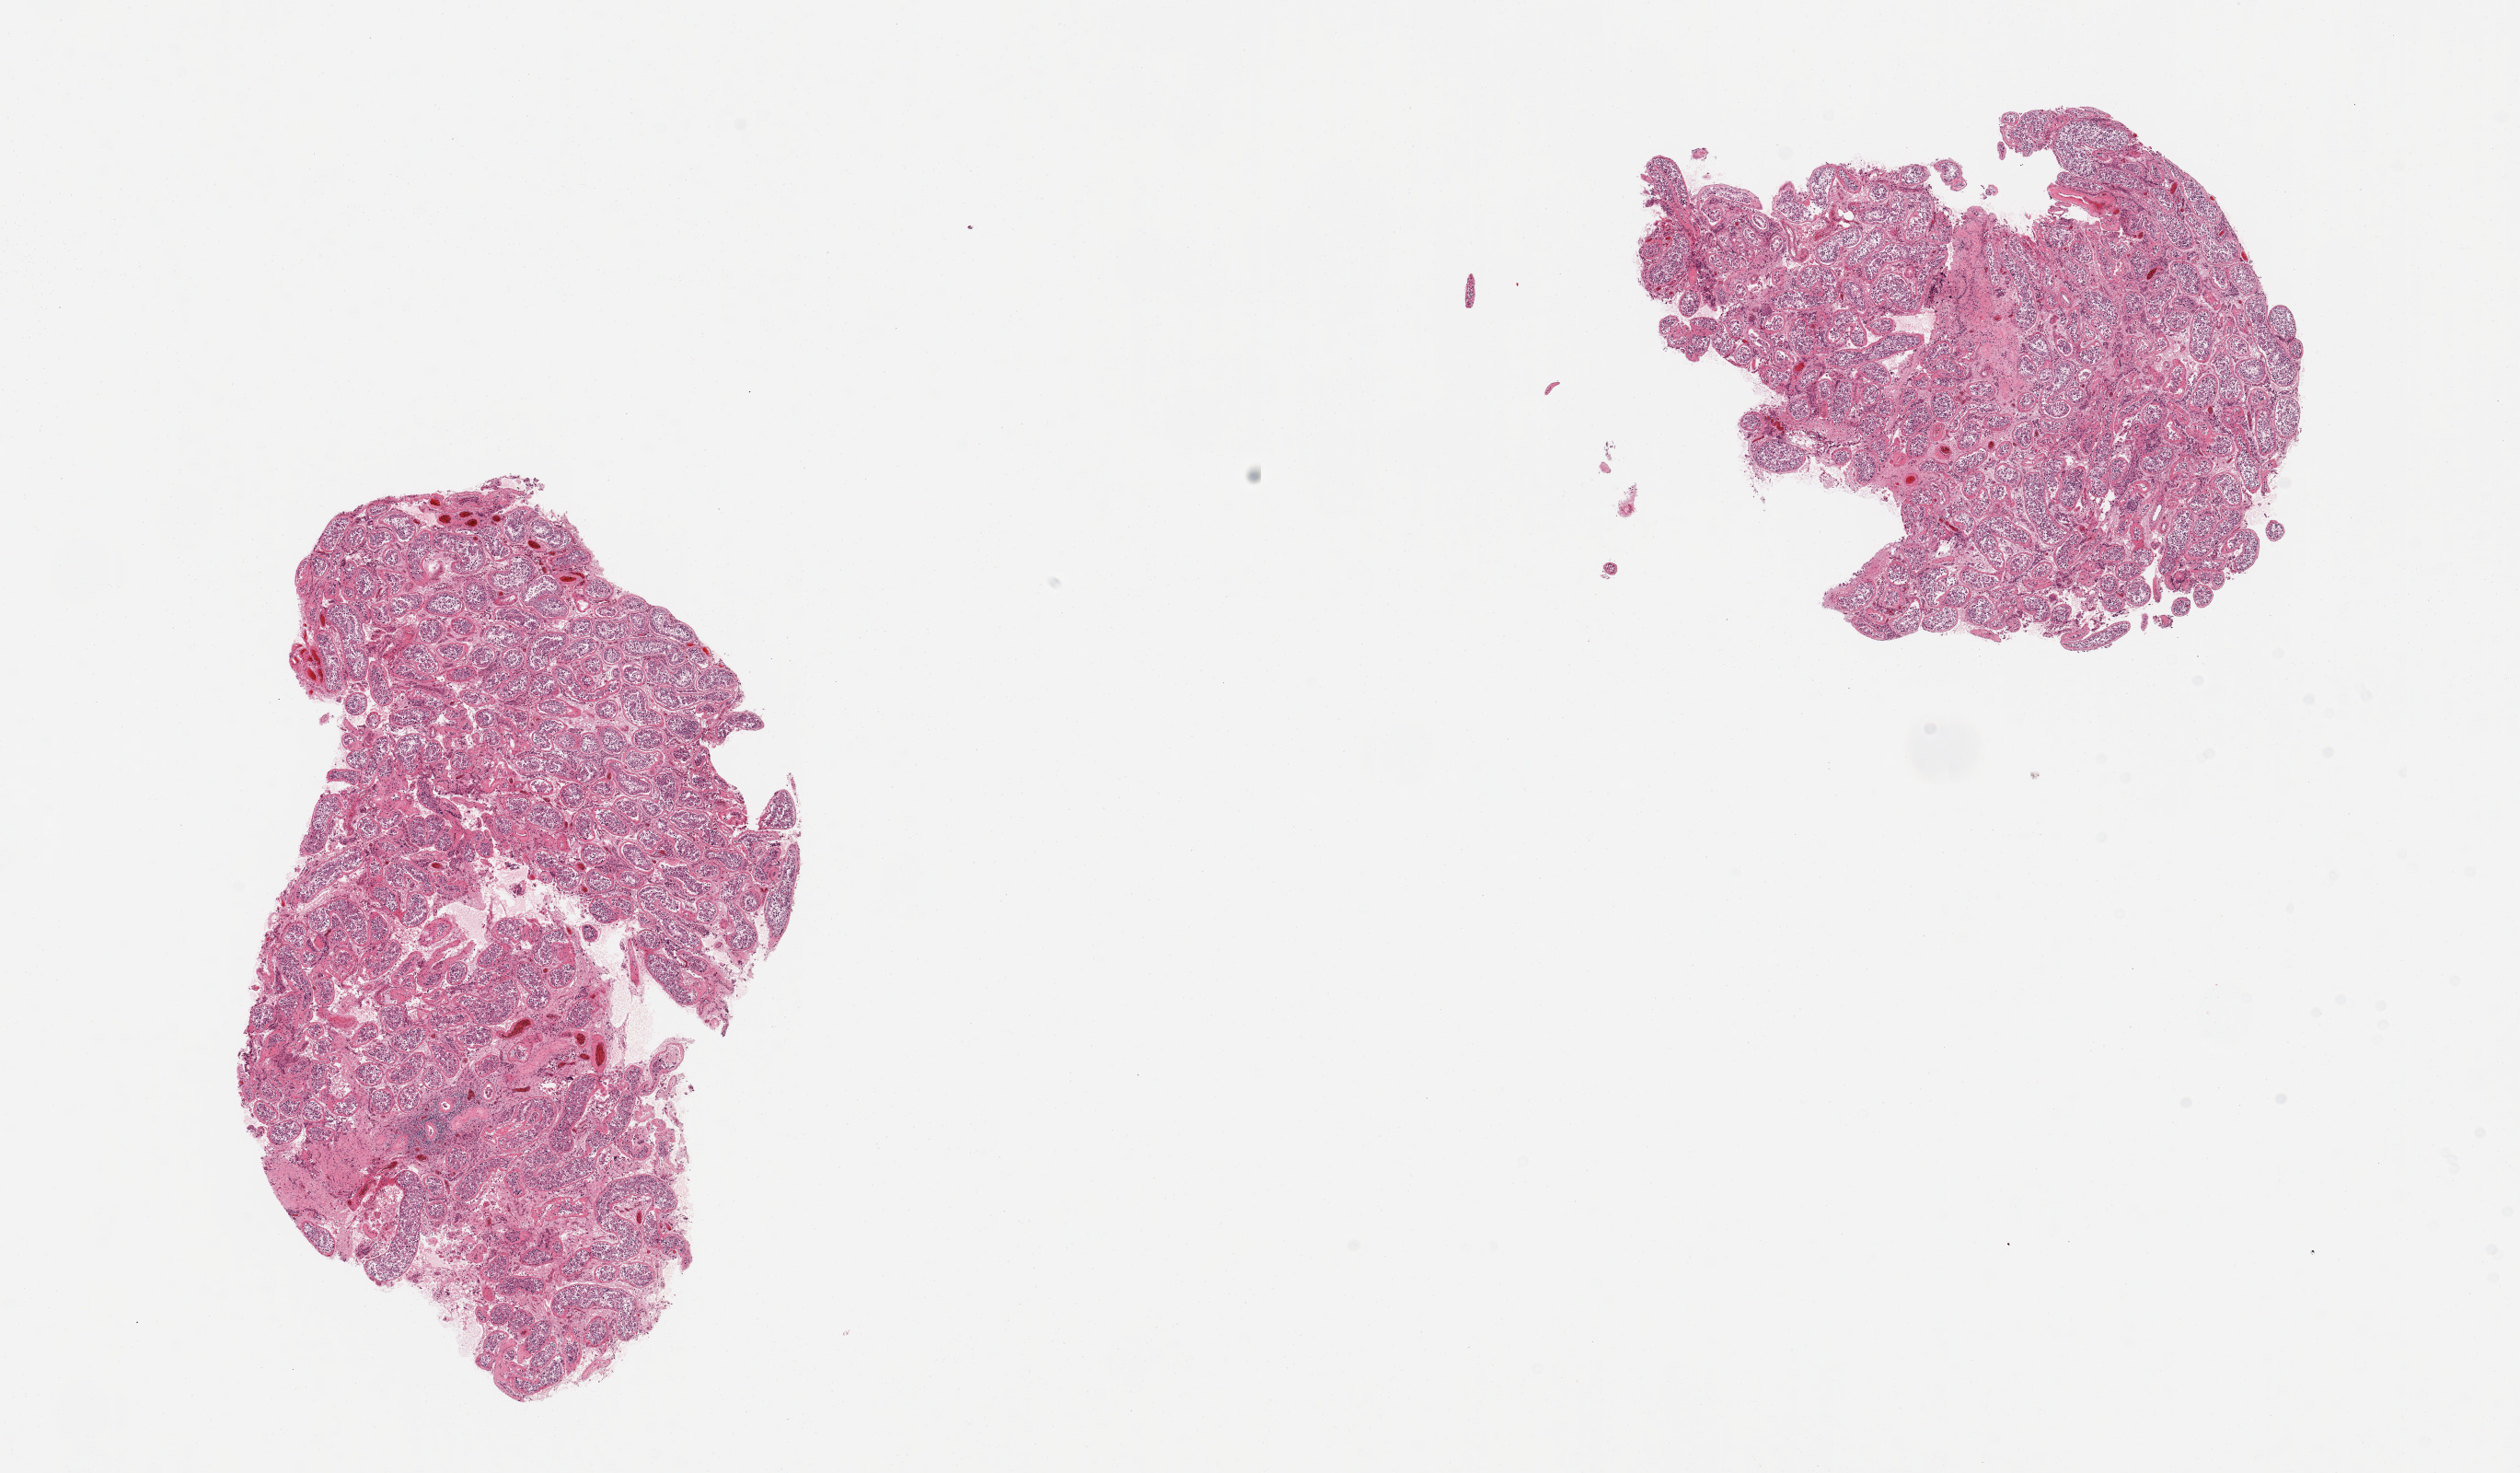
Haematoxylin and eosin whole-slide image, a low-resolution overview of the entire scanned area, about 21.7 x 12.7 mm (acquisition: 20x scan); PAXgene-fixed paraffin-embedded (PFPE) section; target tissue: testis; donor tissue sample. Donor sex: male.
Reviewer comment on this tissue sample: 2 pieces, tubular cells badly autolyzed, sloughing into lumen.